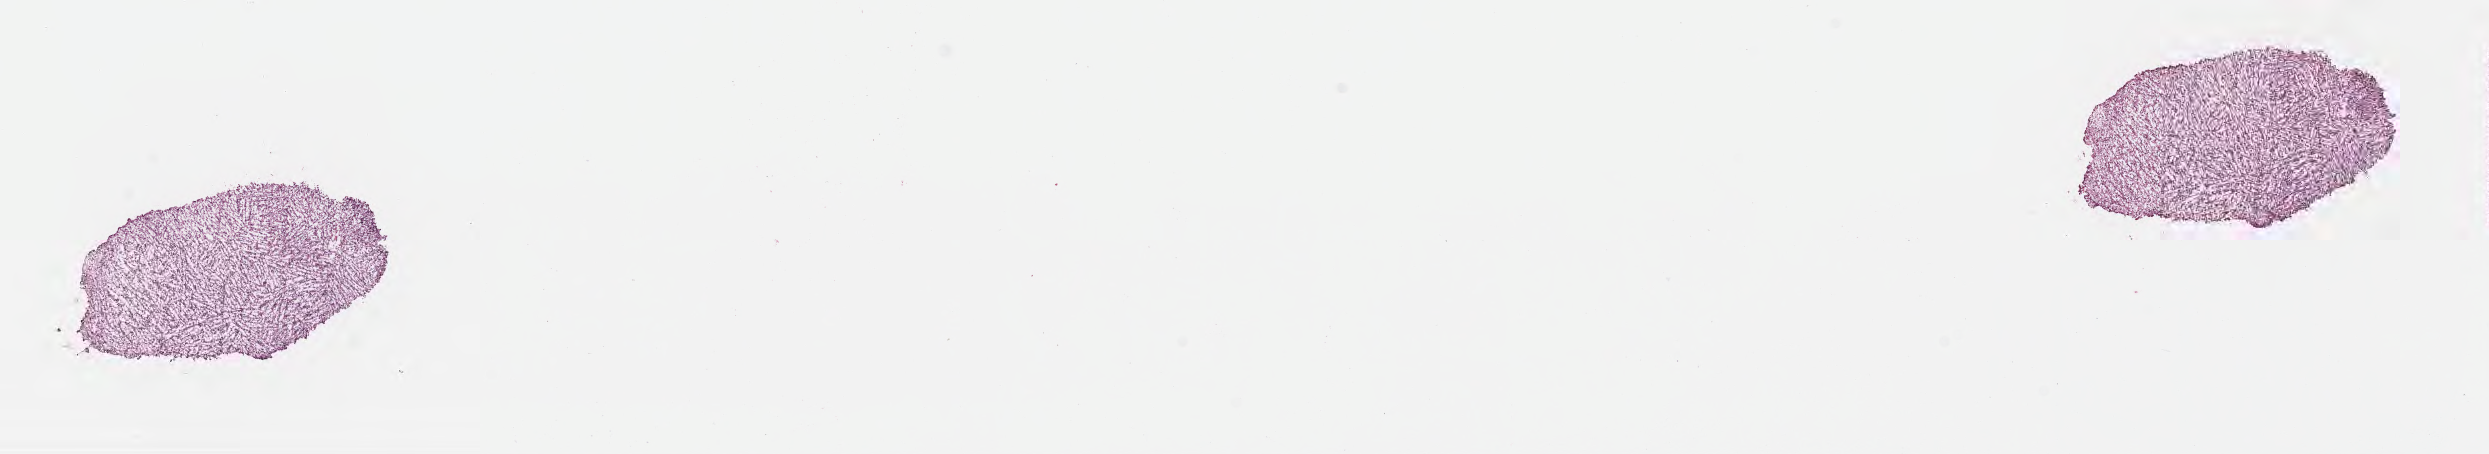
H&E whole-slide image, a low-resolution overview of the entire scanned area, about 20.1 x 3.7 mm; frozen section (tissue freezing medium); recurrent tumor; site: brain. Male, age 50 years at initial diagnosis. Composition of this section per pathologist review: tumor cells 79%, tumor nuclei 90%, stromal cells 13%, necrosis 0%, normal cells 8%. Infiltration values recorded for this section: lymphocyte infiltration 0%, monocyte infiltration 0%, neutrophil infiltration 0%.
Section: top of the tissue portion. Patient diagnosis: Glioblastoma, NOS.